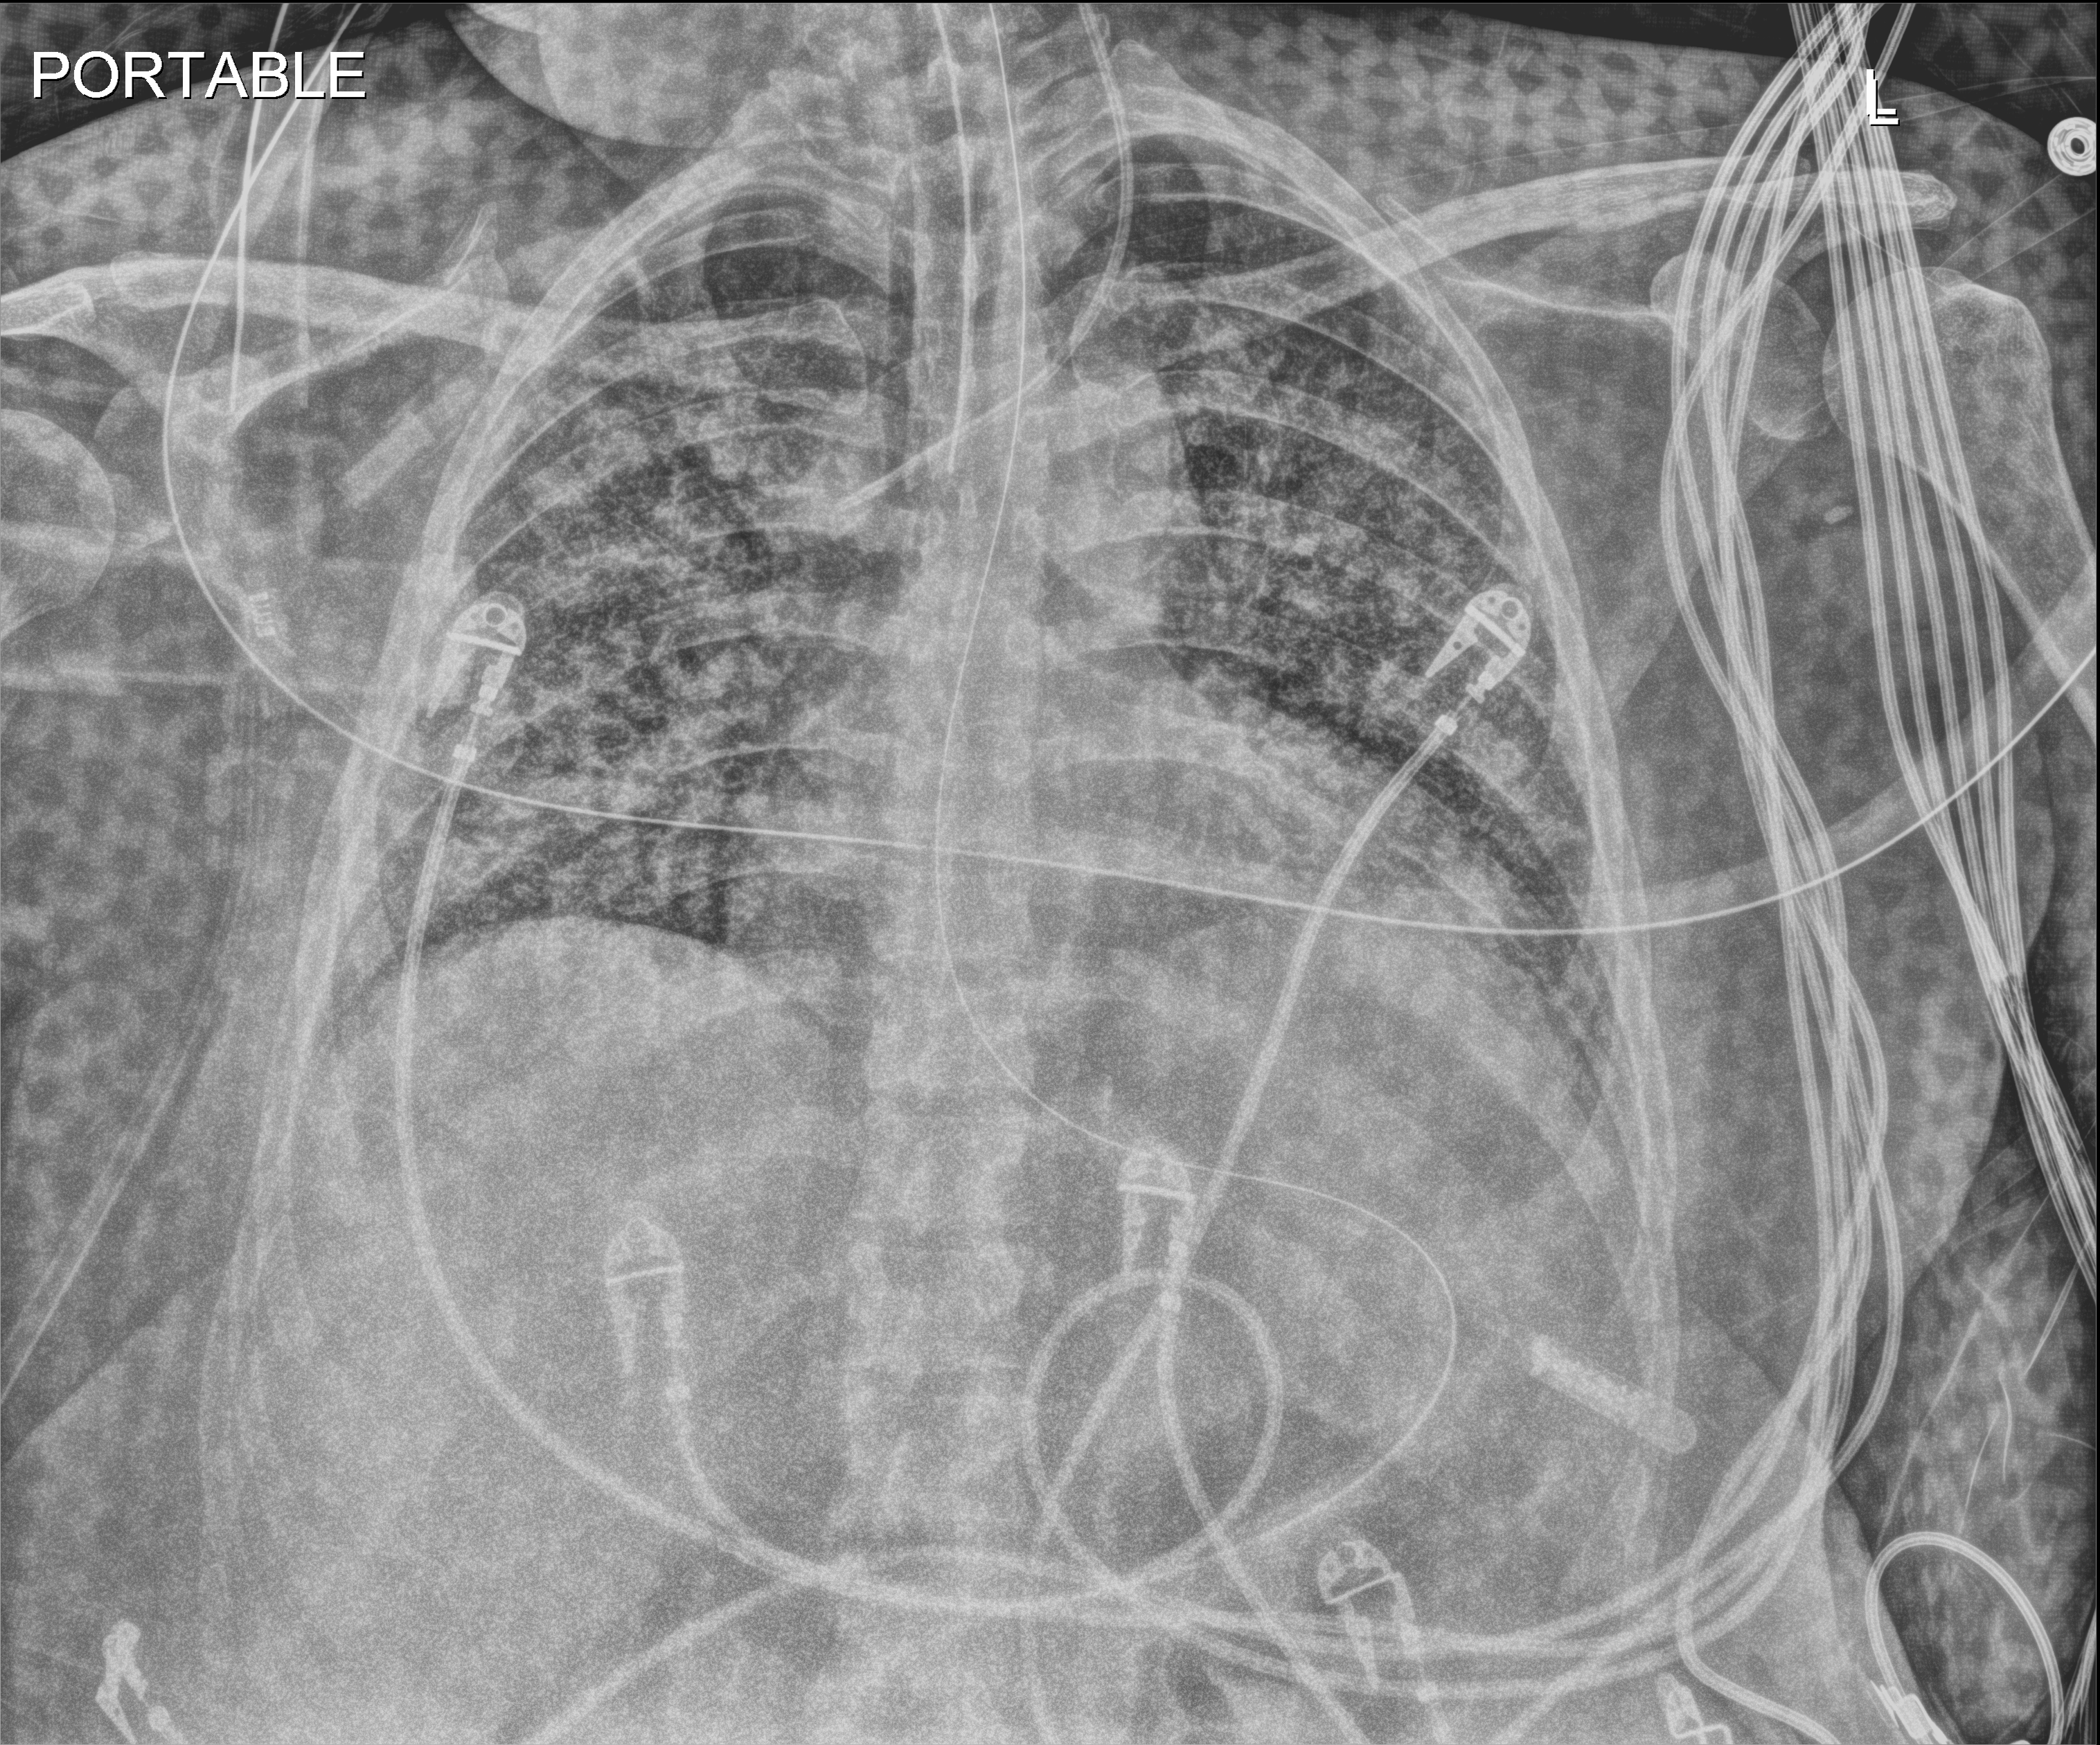
Chest X-ray. Female patient hospitalised with COVID-19, age 18–59 years.
From the hospital-stay record, not from the radiograph (when in the stay this image was taken is not recorded):
- mechanically ventilated during this hospital stay: yes